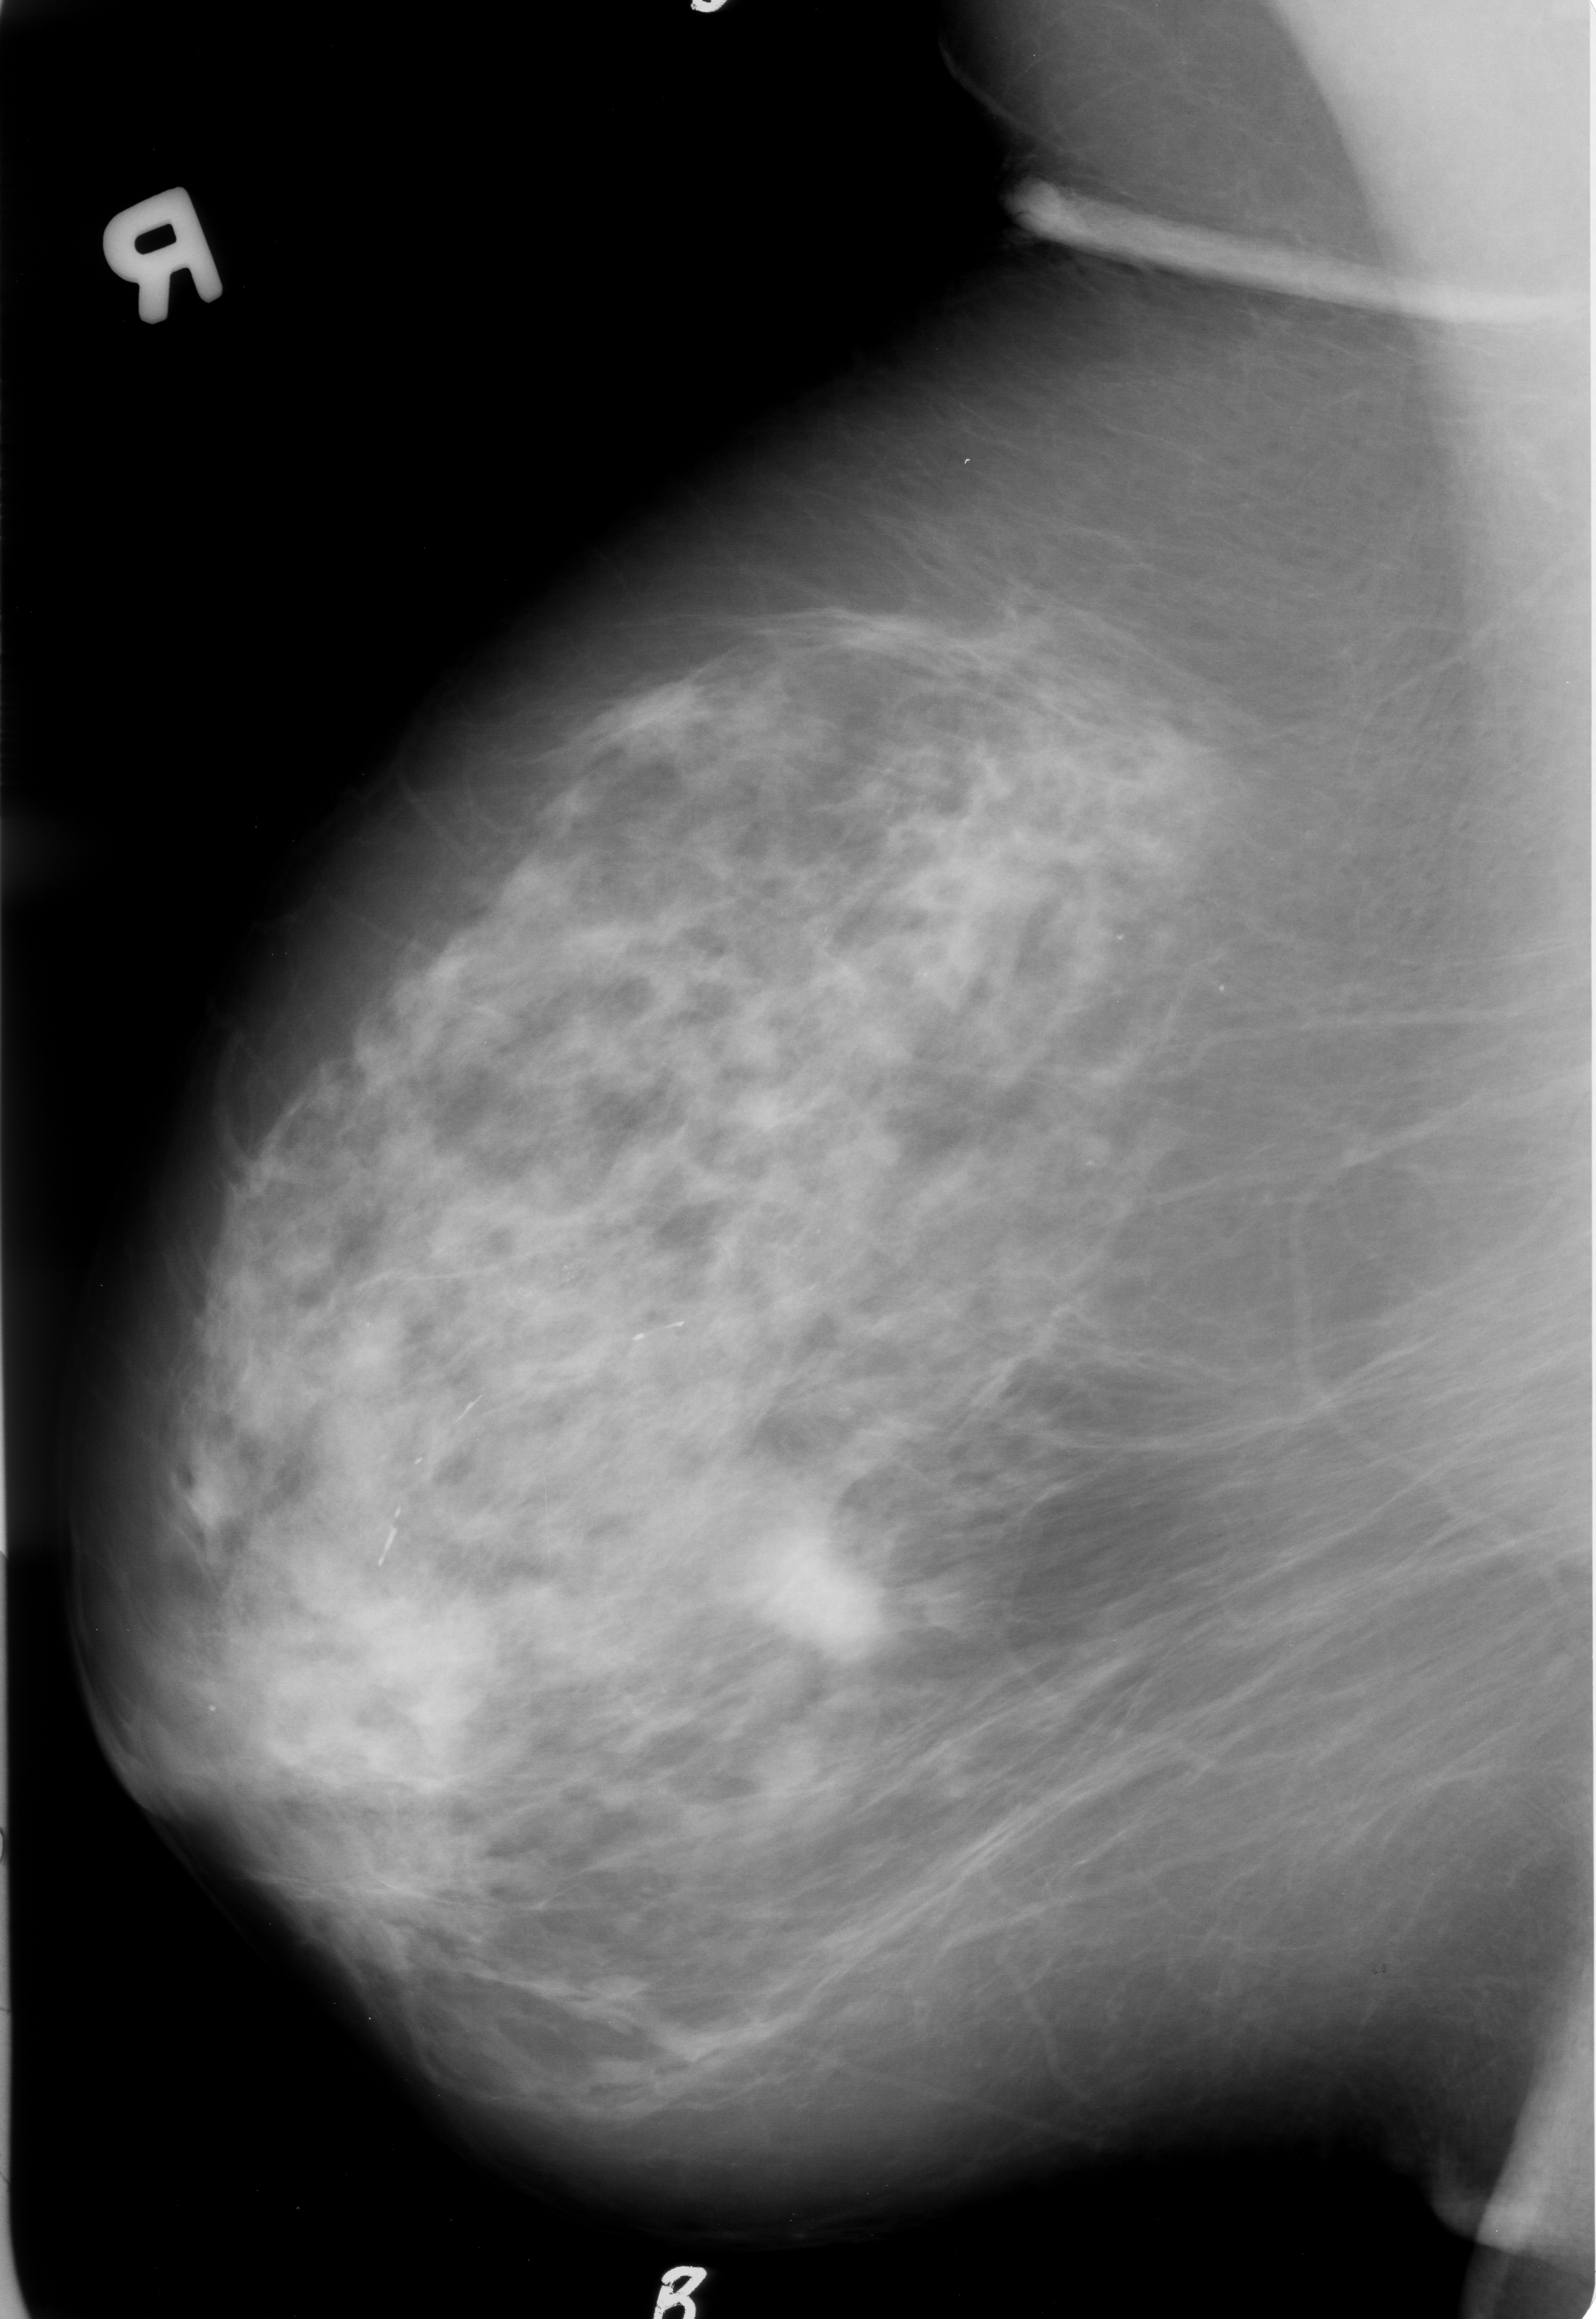
Scanned film-screen mammogram. Right breast. MLO view. 1596 × 2319 image matrix.
Expert-marked regions of interest on this image (one box per marked abnormality):
- mass, shape irregular / architectural distortion, margins obscured / spiculated; BI-RADS assessment category 5; pathology result (as recorded, not read from the image): malignant: bounding box (x1, y1, x2, y2) in pixels: (735, 1530, 885, 1661)